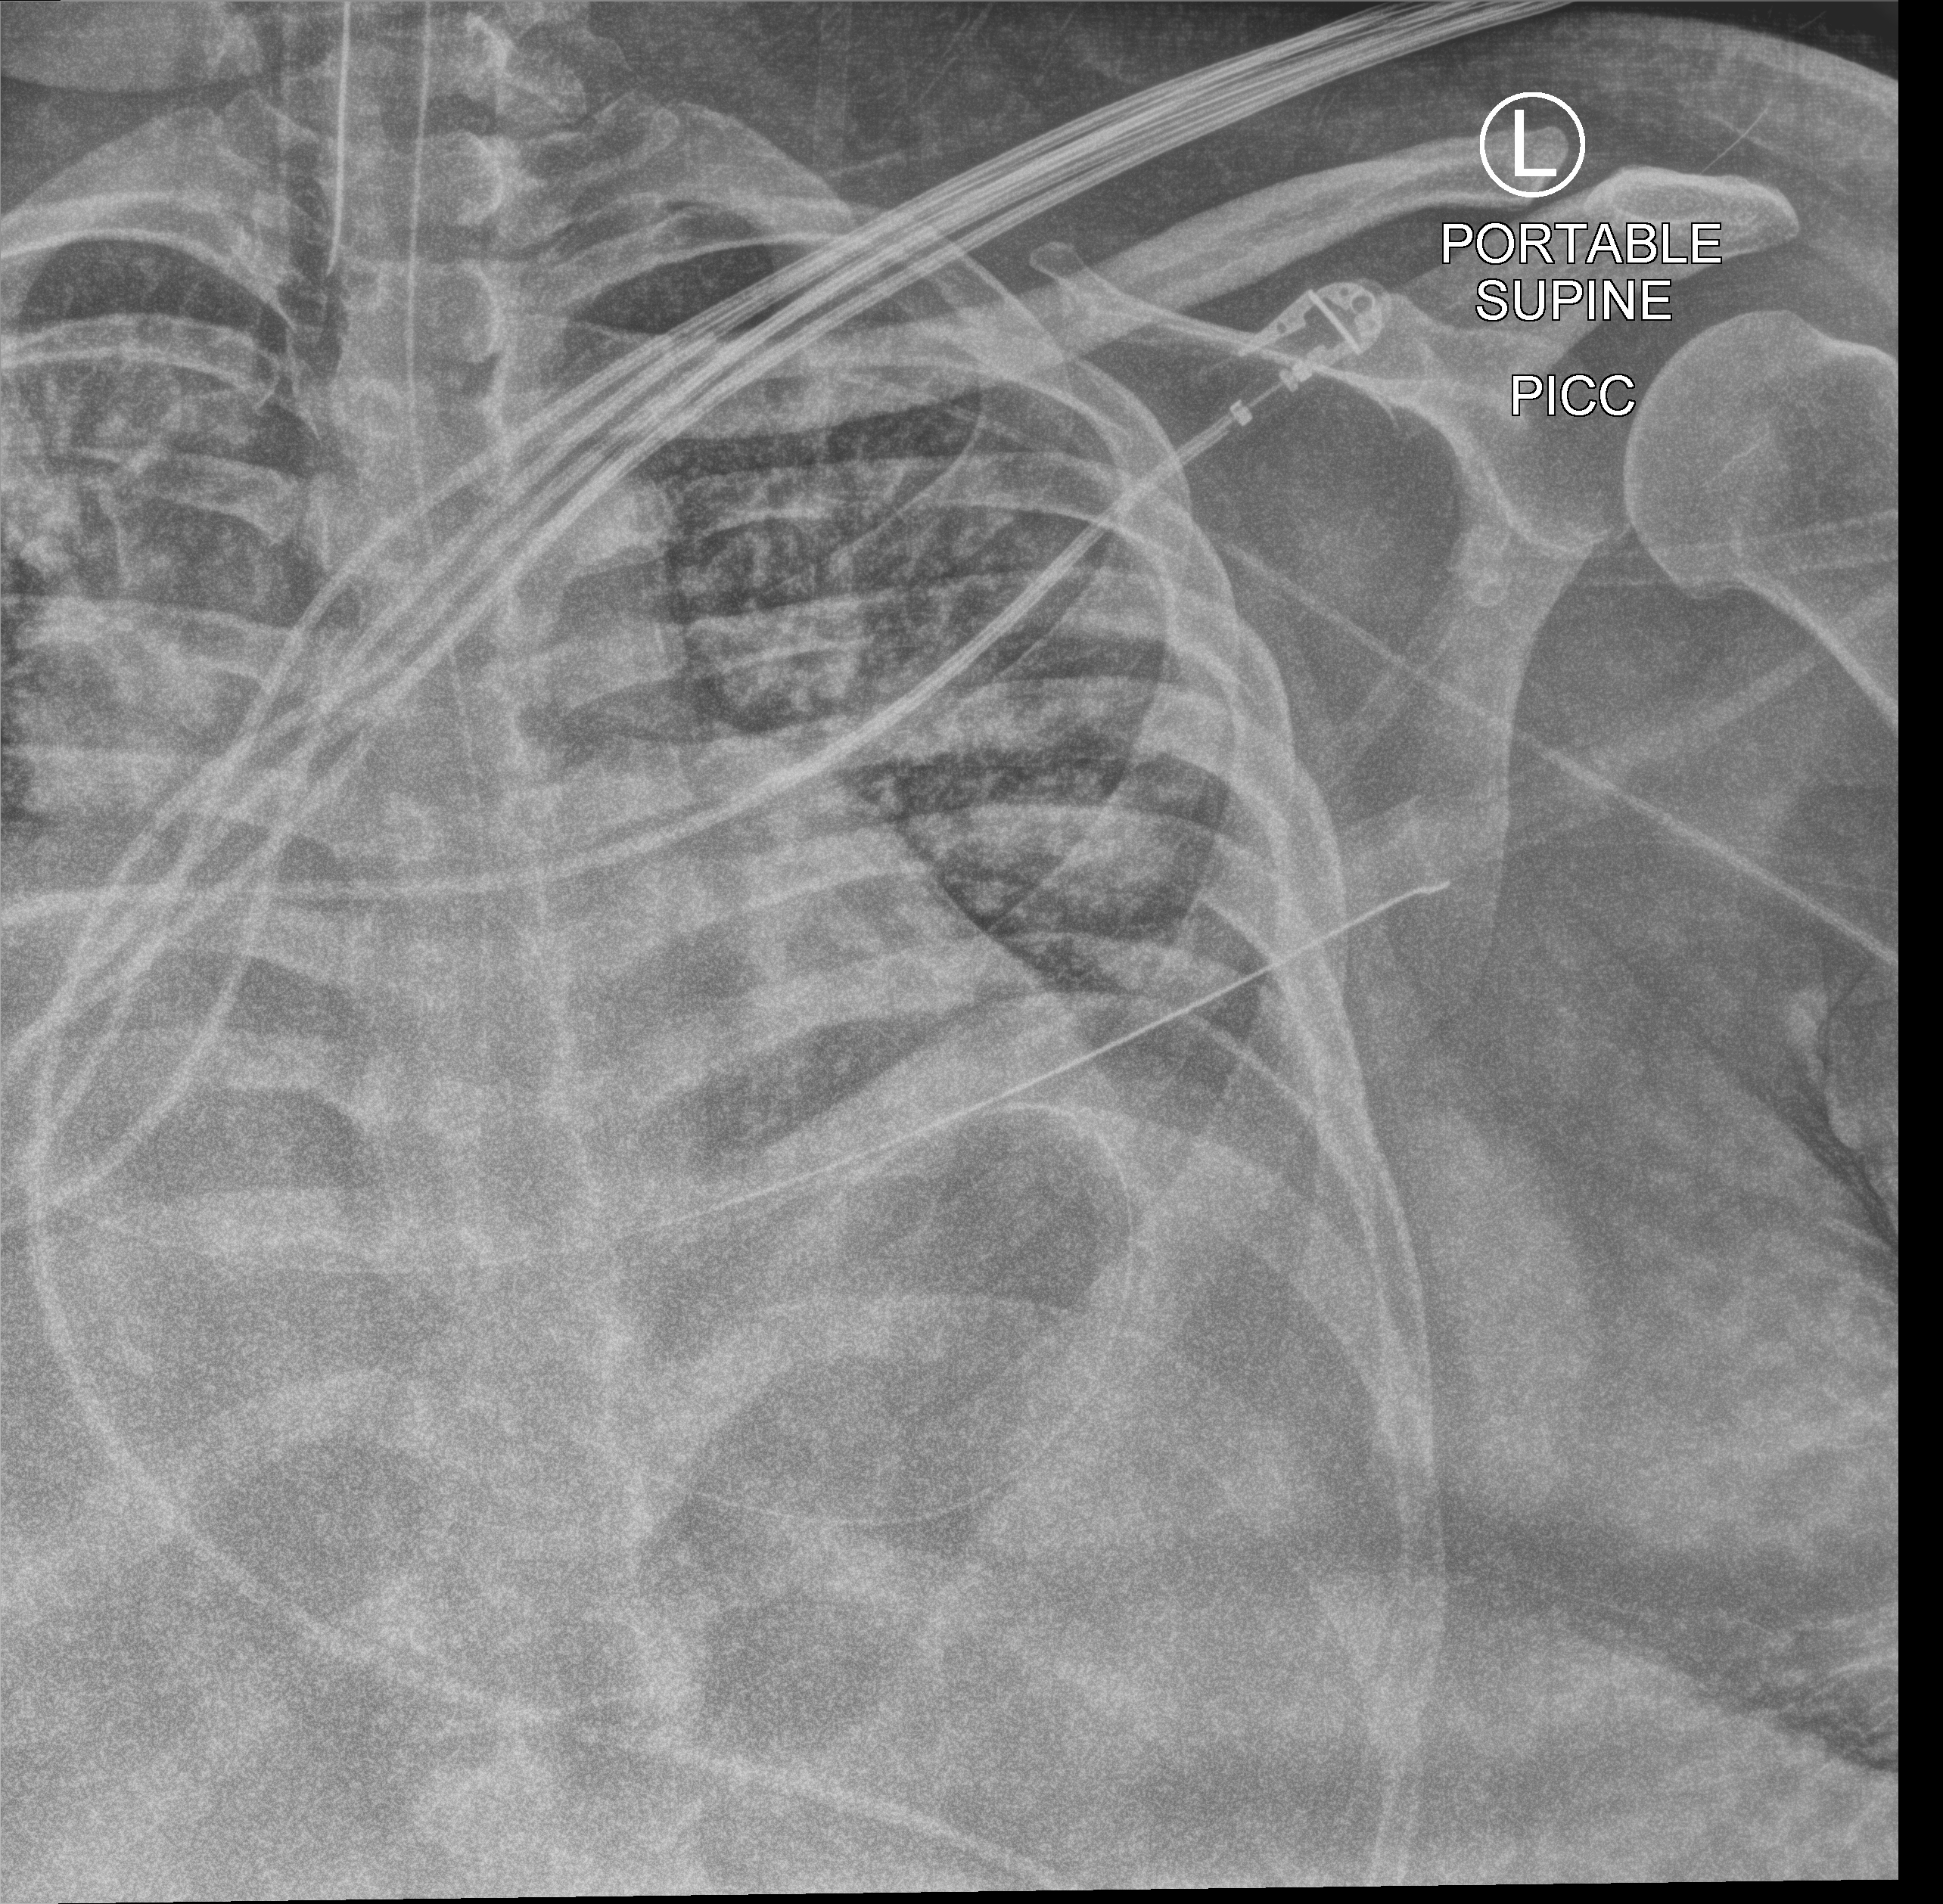
Chest X-ray (portable), anteroposterior (AP) projection. Patient hospitalised with COVID-19; male, aged 18–59 years.
Admission-level facts for this patient (not findings on this image; timing relative to this image not recorded):
- other chronic lung disease (admission record): yes
- admitted to intensive care during this hospital stay: yes